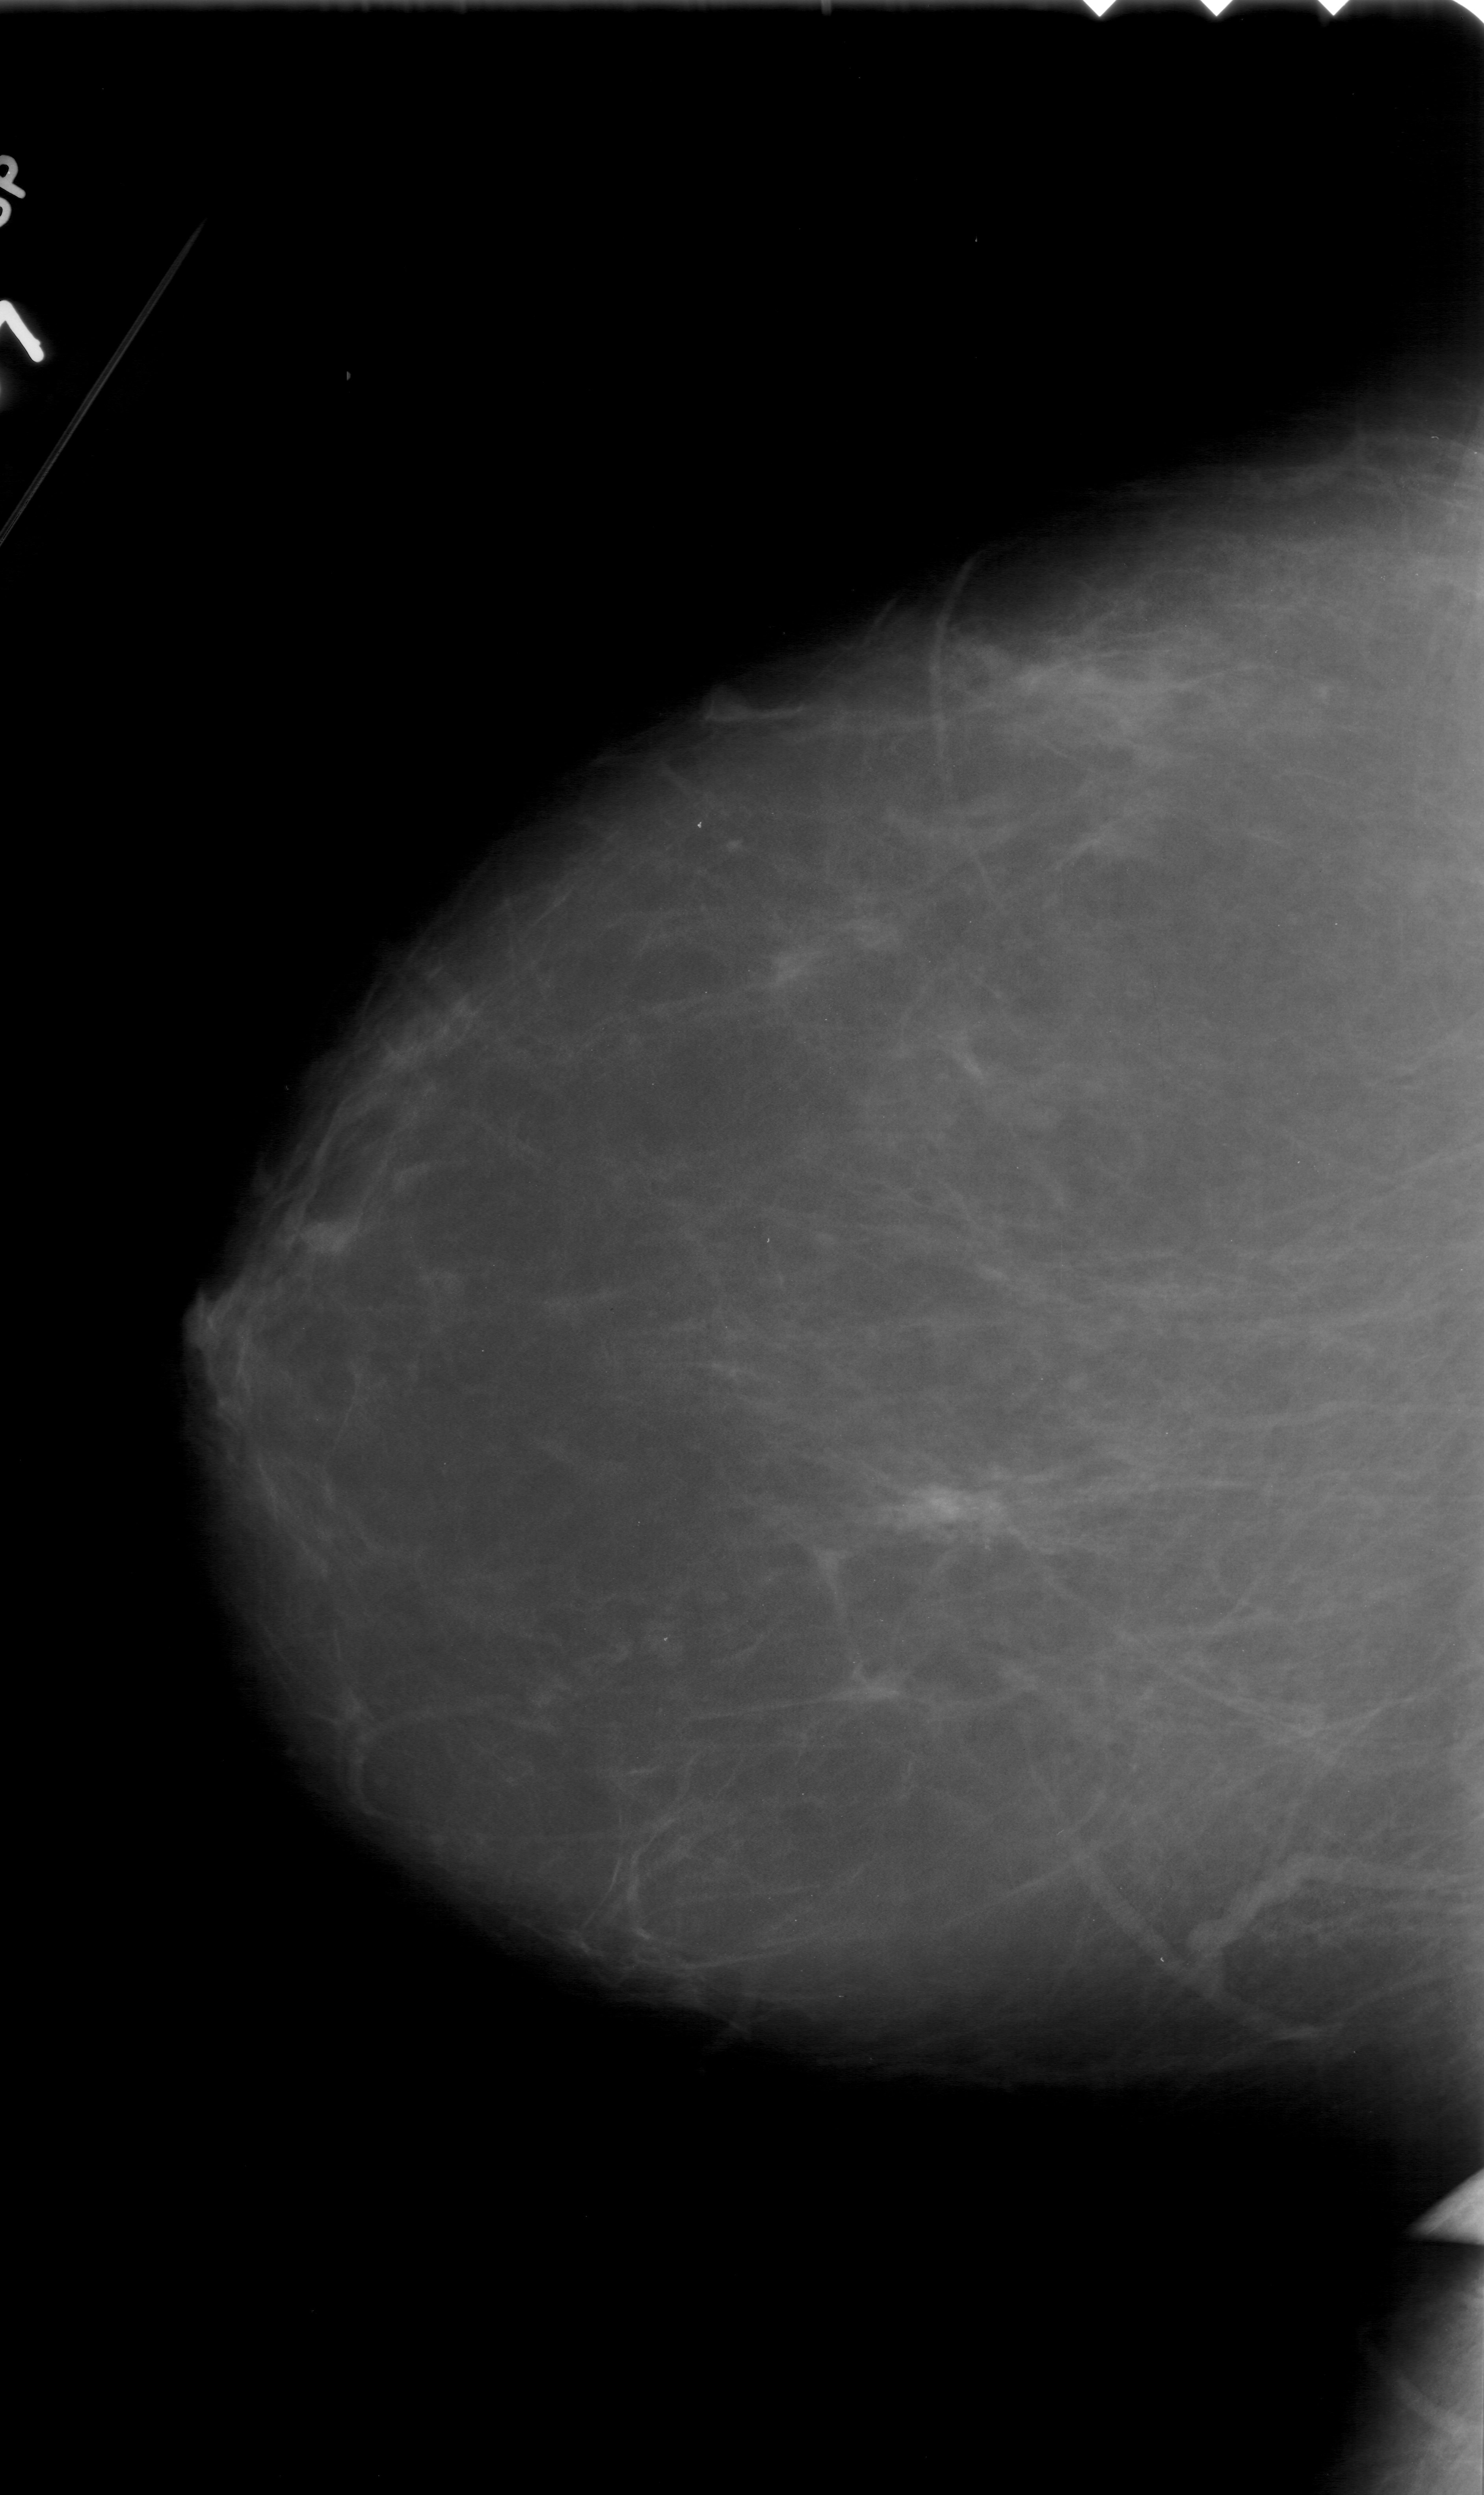
Mammogram (digitized film); left breast; craniocaudal (CC) view; breast composition: scattered fibroglandular densities (BI-RADS density category 2 of 4).
- Abnormality record for this image: calcifications, morphology pleomorphic, distribution clustered; BI-RADS assessment category 4; pathology (as recorded): malignant.